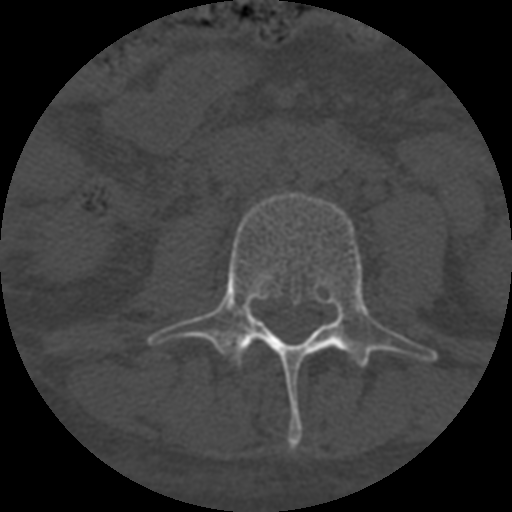
CT including the spine, one axial slice; slice 236 of 708 in the series (ordered by position); one of 3 acquisitions stored at this slice position; bone window (W 1800 / L 400 HU); 1.25 mm slice thickness; 512 × 512 image matrix, field of view 160 × 160 mm. Patient age 55 years. From the clinical record (not read from this slice): primary cancer: colon; vertebrae with lytic lesions (as recorded): T12, L1, L5.
Structures marked on this image (semi-automatically segmented with operator editing):
- L3 vertebra: box from (x=147, y=193) to (x=438, y=448) px